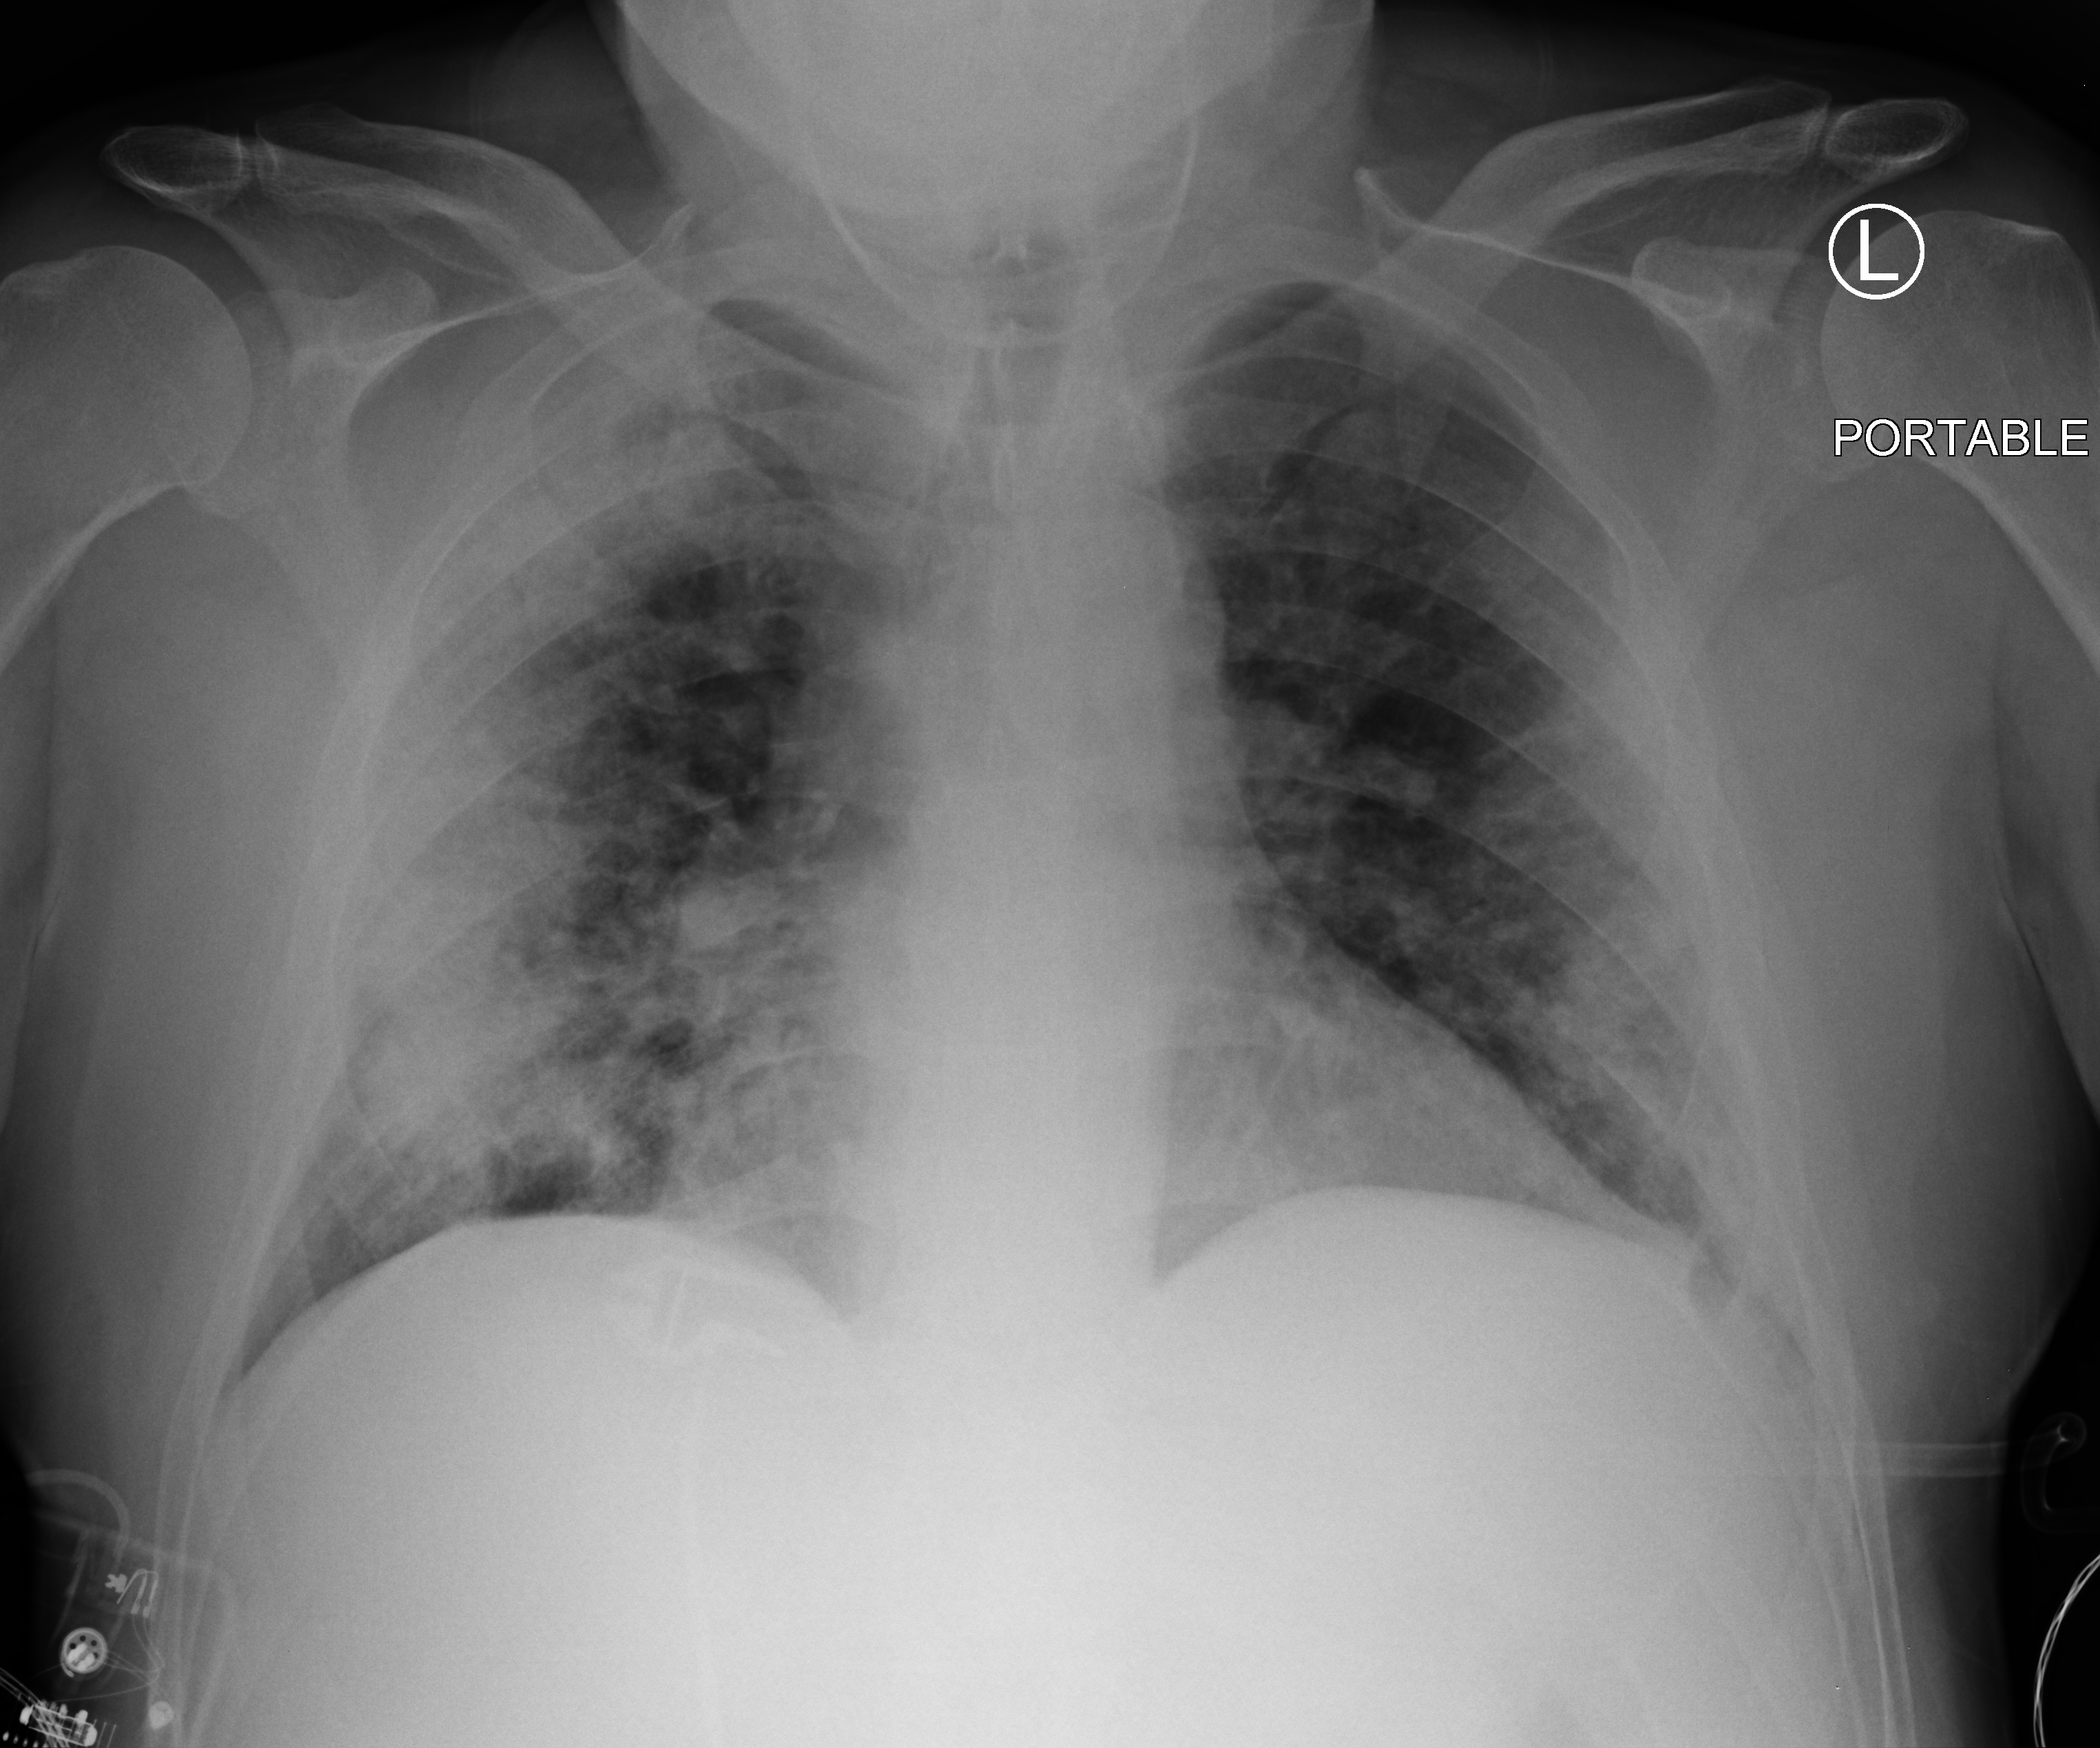
Chest X-ray (portable); anteroposterior (AP) projection. Patient hospitalised with COVID-19; male, aged 60–74 years.
From the hospital-stay record, not from the radiograph (when in the stay this image was taken is not recorded):
- length of hospital stay: 12 days
- mechanically ventilated during this hospital stay: no
- admitted to intensive care during this hospital stay: no